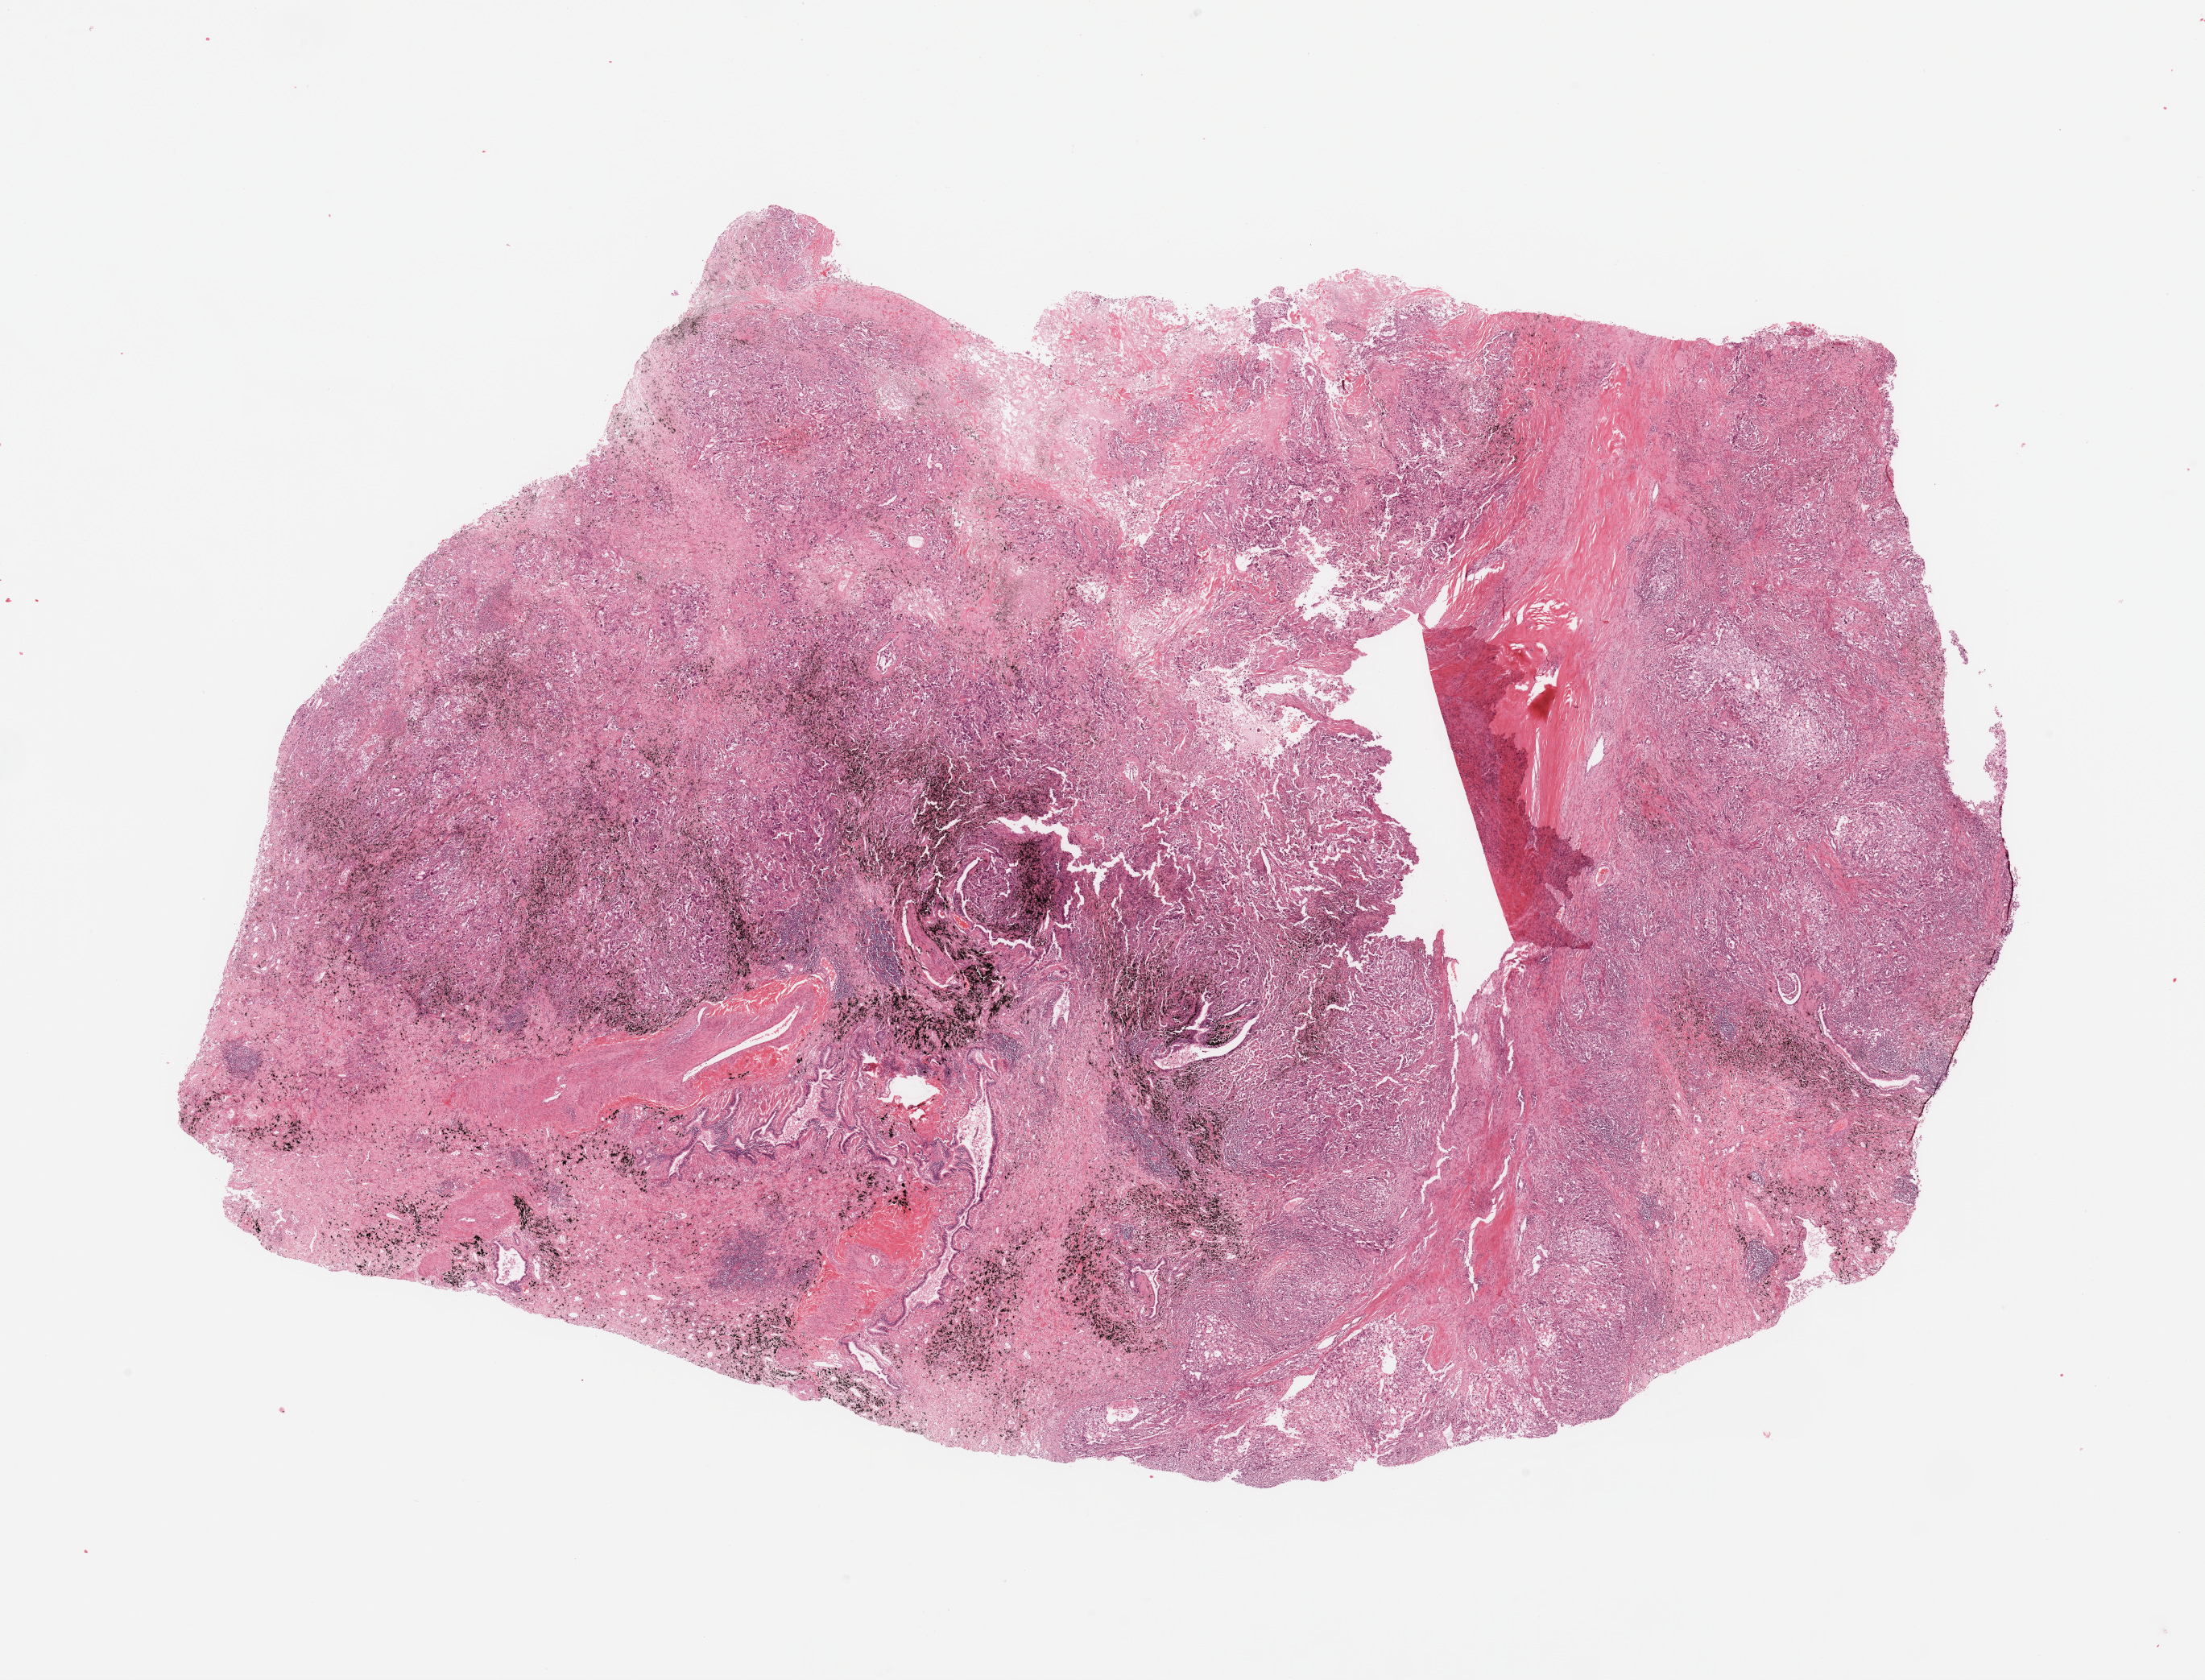
Digitized H&E-stained tissue section (whole slide), a low-resolution overview of the entire scanned area, about 21.7 x 16.5 mm (slide scanned at 20x). Lung, tumour tissue. Patient: male, age 69 years.
Histologic diagnosis: Adenocarcinoma, NOS.